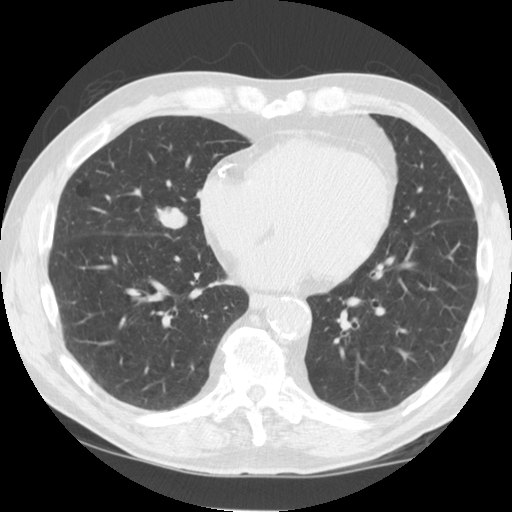
Low-dose screening chest CT, one axial slice. Slice 43 of 125 in the series (ordered by position). Reconstruction kernel STANDARD. 120 kVp. Lung window (W 1500 / L -600 HU). 2.5 mm slice thickness. 512 × 512 image matrix, field of view 350 × 350 mm.
Annotated regions visible in this slice (manually delineated by an expert):
- lesion 1 (tumor, middle lobe of right lung): bounding box <157,208,187,229> (left, top, right, bottom; pixels)